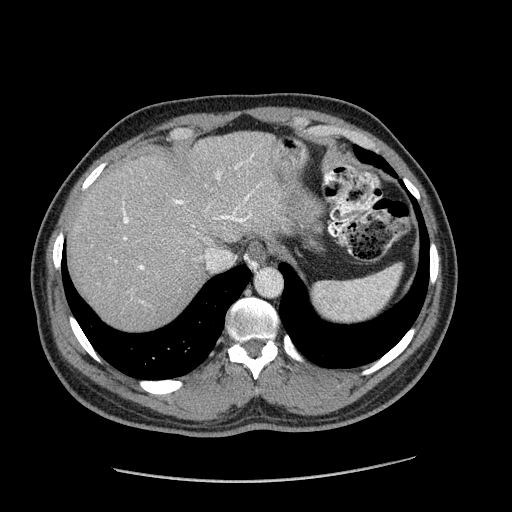
Contrast-enhanced abdominal CT (liver protocol), one axial slice; position 145 of 182 along the scan axis; reconstruction kernel STANDARD; 120 kVp; soft-tissue window (W 400 / L 40 HU); 2.5 mm slice thickness; 512 × 512 image matrix, field of view 400 × 400 mm. From the clinical record (not read from this slice): diagnosis: hepatocellular carcinoma (patient treated with transarterial chemoembolisation; whether this scan precedes or follows treatment is not stated here); TNM stage (as recorded): Stage-I; Child-Pugh class: A; tumour differentiation: well differentiated; tumour nodularity: uninodular.
Outlined on this slice (semi-automatic segmentation, software-assisted and operator-edited):
- abdominal aorta: bounding box <257,270,282,297> (left, top, right, bottom; pixels)
- liver parenchyma outside the tumour (the mass and vessels are separate outlines, so this box may not span the whole liver): <68,132,302,328>
- liver vessels: <115,154,259,270>